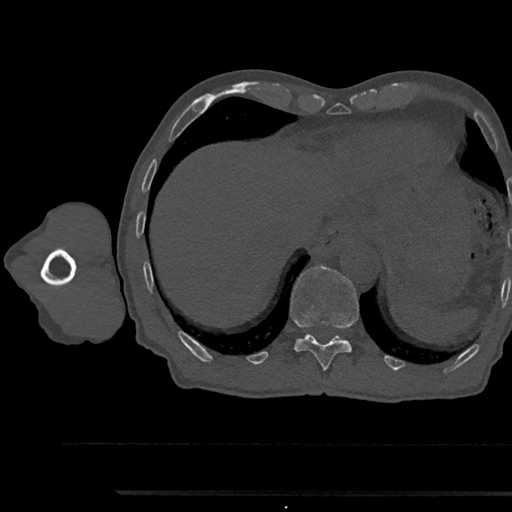
CT including the spine, one axial slice; slice 779 of 797 in the series (ordered by position); reconstruction kernel Br40s/3; 120 kVp; bone window (W 1800 / L 400 HU); 0.5 mm slice thickness; 512 × 512 image matrix, field of view 367 × 367 mm. Patient: male, 79 years. Case-level facts recorded for this patient, not image findings: primary cancer: prostate.
Annotated regions visible in this slice (semi-automatic segmentation, software-assisted and operator-edited):
- T11 vertebra: bounding box <290,266,359,371> (left, top, right, bottom; pixels)